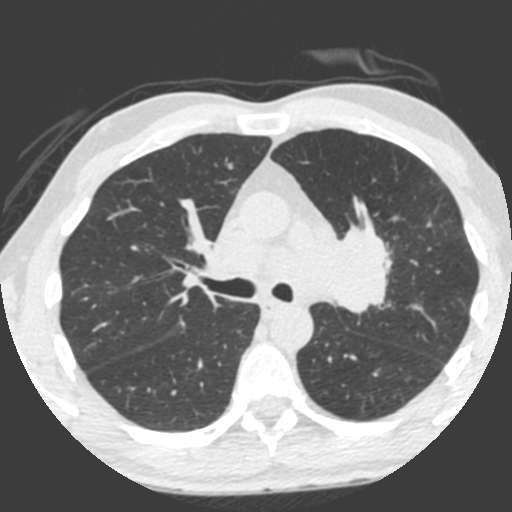
Low-dose screening chest CT, one axial slice; slice 140 of 212 in the series (ordered by position); lung window (W 1500 / L -600 HU); 2 mm slice thickness; 512 × 512 image matrix, field of view 315 × 315 mm.
Annotated regions visible in this slice (outlined manually by an expert reader):
- lesion 1 (tumor, upper lobe of left lung): box from (x=328, y=224) to (x=392, y=313) px